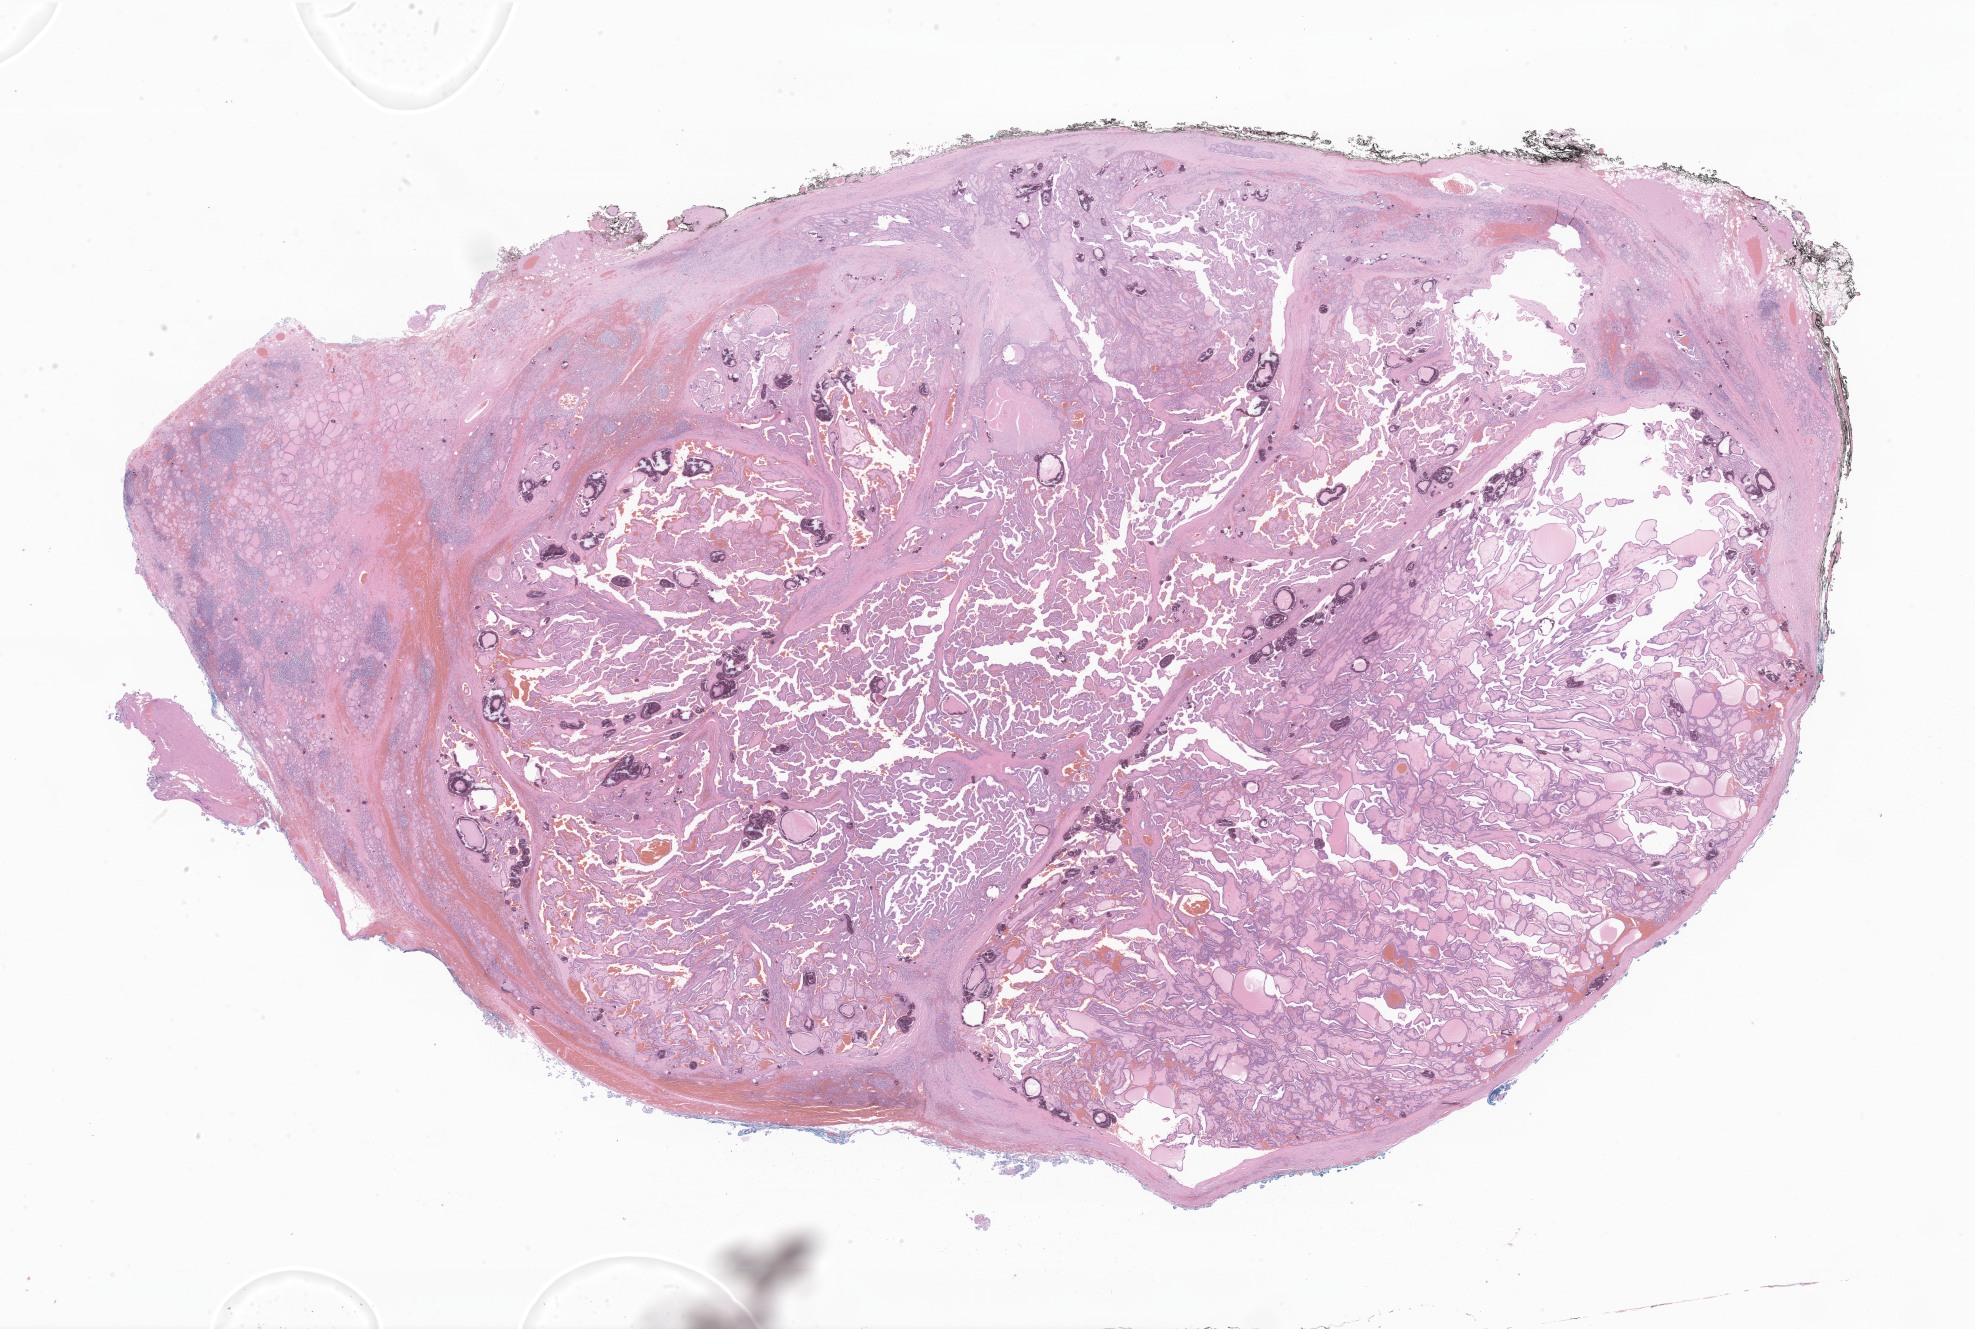
Whole-slide image, H&E stain of tumor tissue from the thyroid, a low-resolution overview of the entire scanned area, about 33.3 x 22.4 mm, FFPE section. Female patient, age 186 months (15 years 6 months).
Diagnosis (ICD-O-3 morphology term): Papillary carcinoma, NOS.